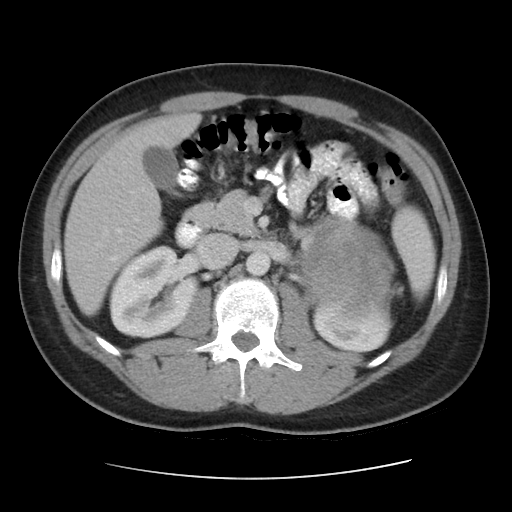
Contrast-enhanced abdominal CT, one axial slice. Position 22 of 48 along the scan axis. 120 kVp. Intravenous contrast given. Soft-tissue window (W 400 / L 40 HU). 5 mm slice thickness. 512 × 512 image matrix, field of view 360 × 360 mm. Male patient, age 32 years. From the clinical record (not read from this slice): diagnosis: adrenocortical carcinoma; tumour side: left adrenal; tumour size at pathology: 14 cm; Ki-67 index: 67 %; stage (as recorded): 3.
Outlined on this slice (semi-automatically segmented with operator editing):
- mass: bounding box <304,219,390,314> (left, top, right, bottom; pixels)